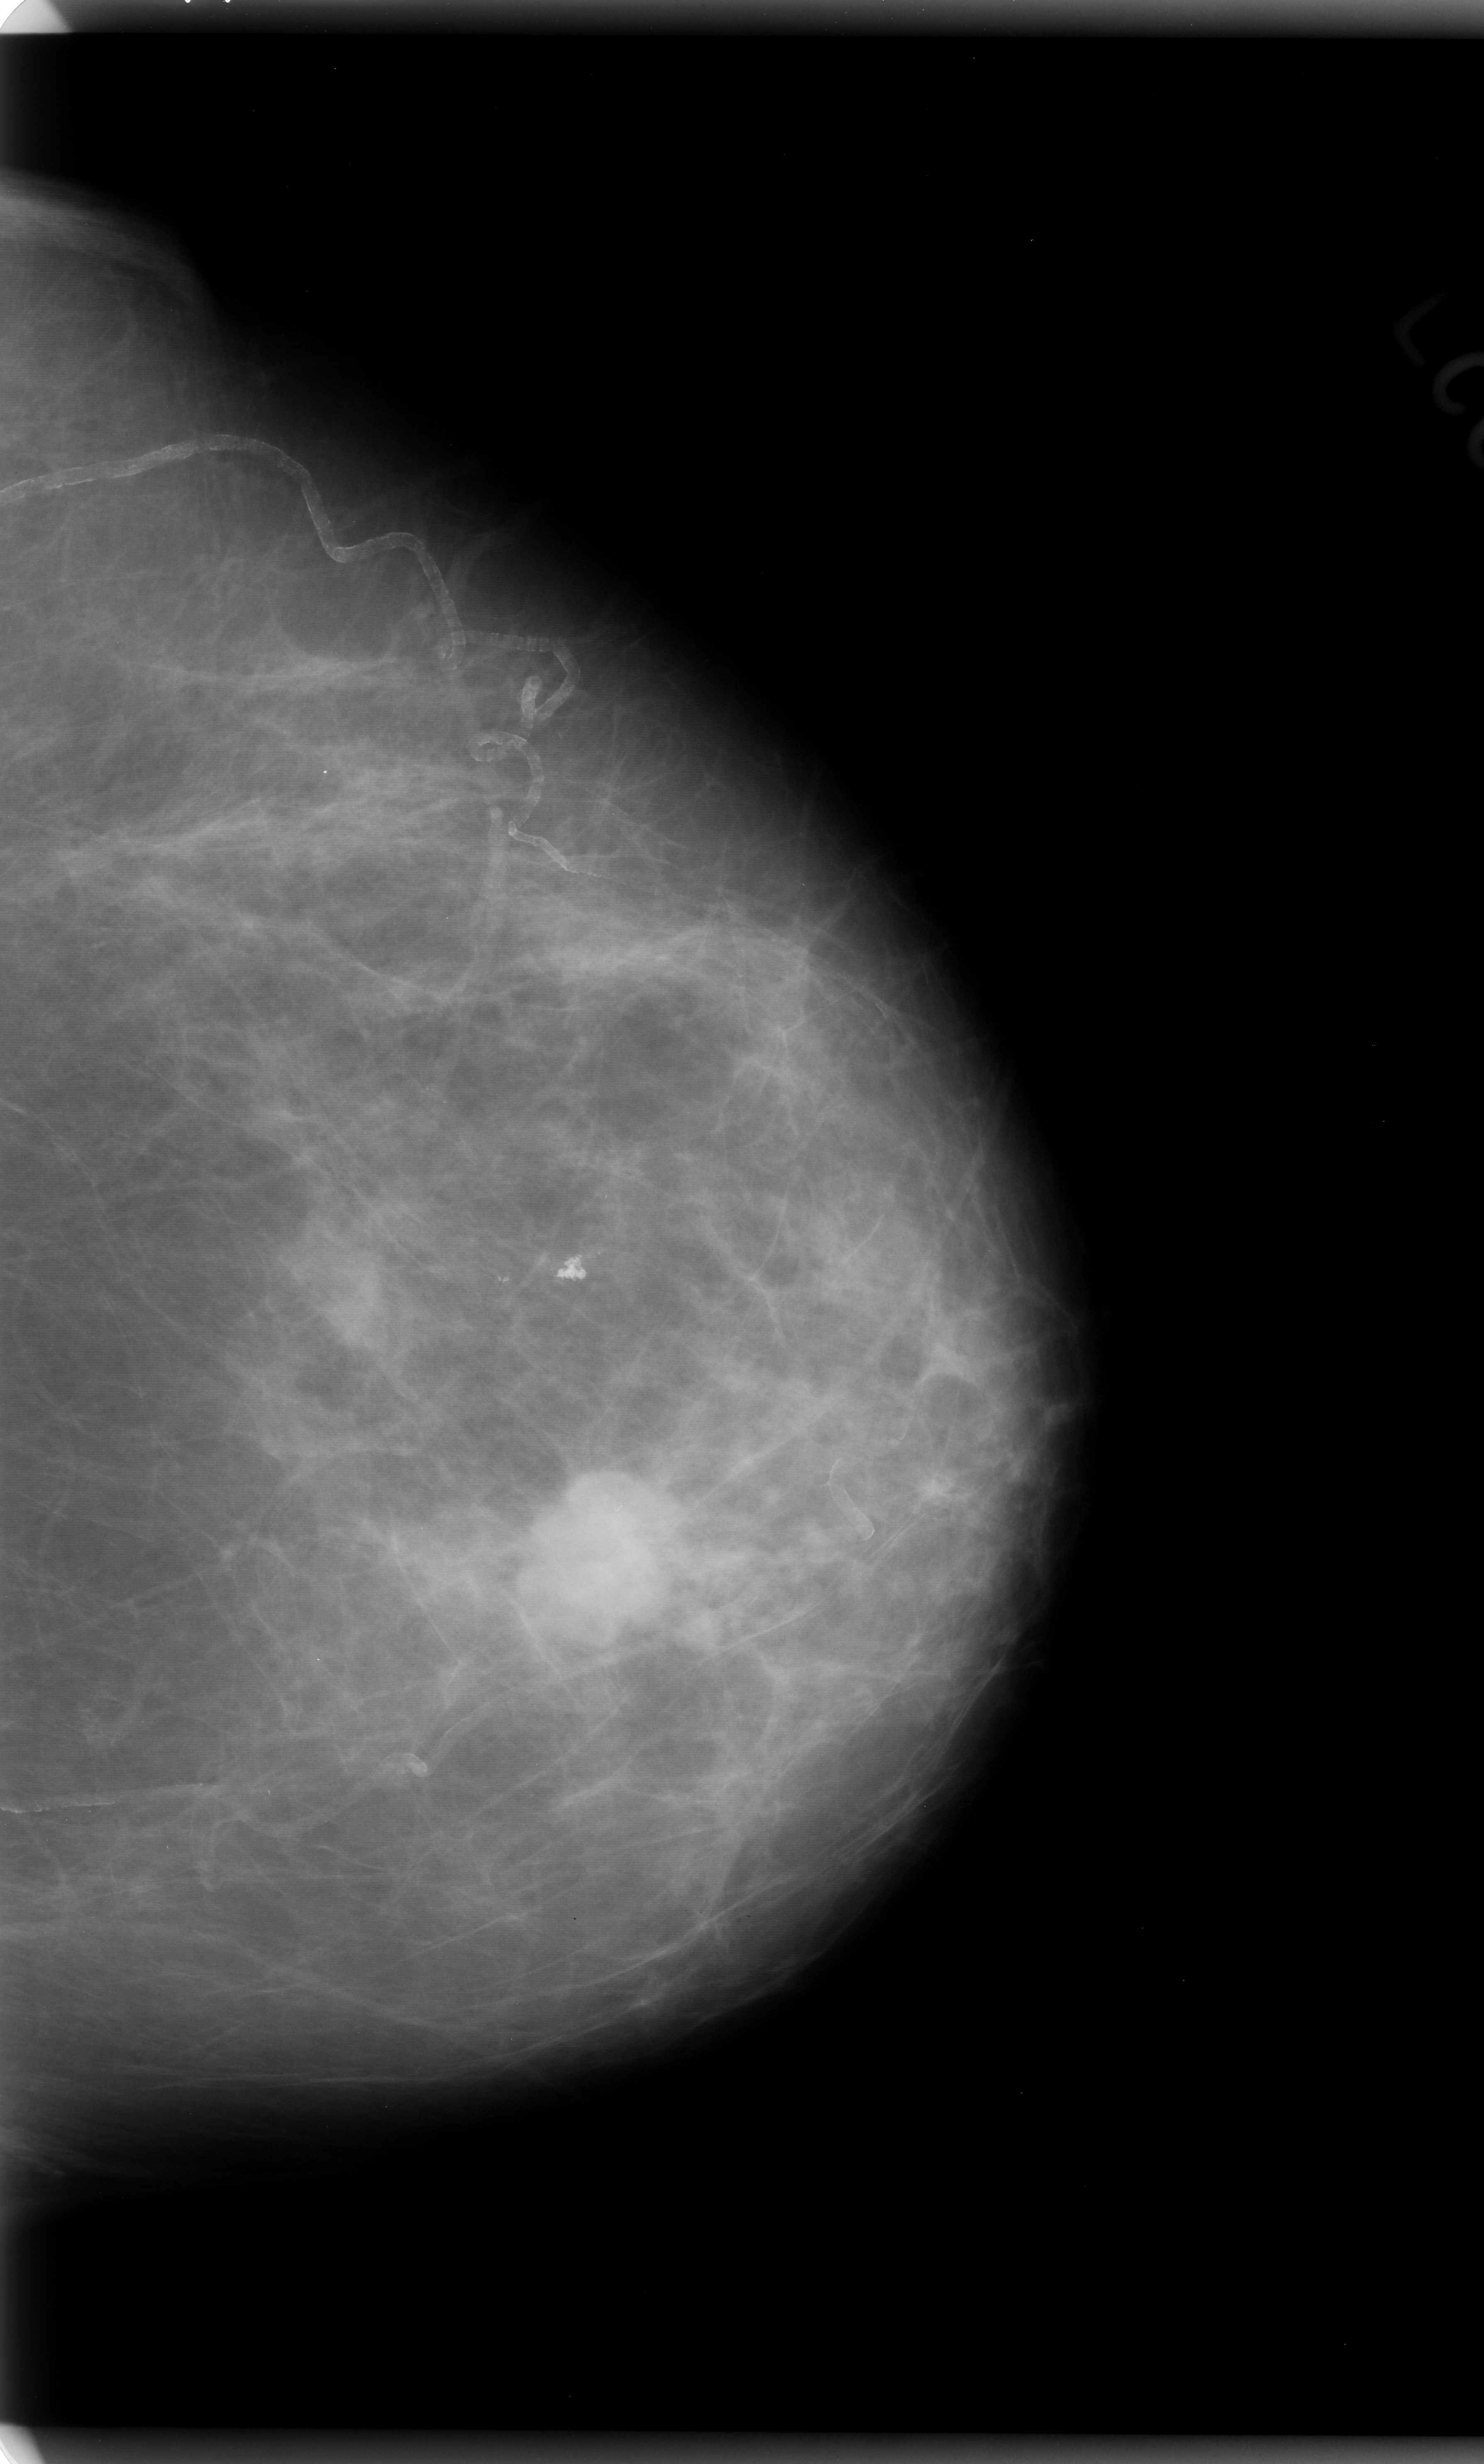
Scanned film-screen mammogram; left breast; craniocaudal (CC) view; breast composition: almost entirely fatty (BI-RADS density category 1 of 4).
Radiologist-marked abnormalities on this image: mass, shape lobulated, margins microlobulated; BI-RADS assessment category 5; subtlety rating 5 on a 1 (subtle) to 5 (obvious) scale; pathology (as recorded): malignant.